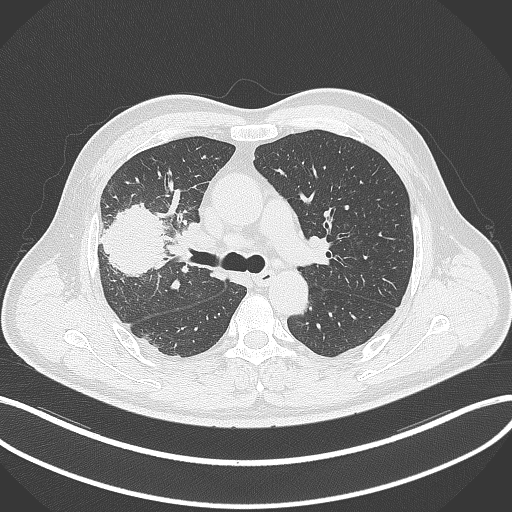
Chest CT, one axial slice. Slice 214 of 348 in the series (ordered by position). 120 kVp. Lung window (W 1500 / L -600 HU). 512 × 512 image matrix, field of view 400 × 400 mm. Male patient, age 55 years. From the clinical record (not read from this slice): clinical TNM (as recorded): T3 N2 M1.
Annotated regions visible in this slice (bounding box drawn by a radiologist):
- lung tumour (recorded histology: adenocarcinoma): box from (x=97, y=203) to (x=165, y=280) px